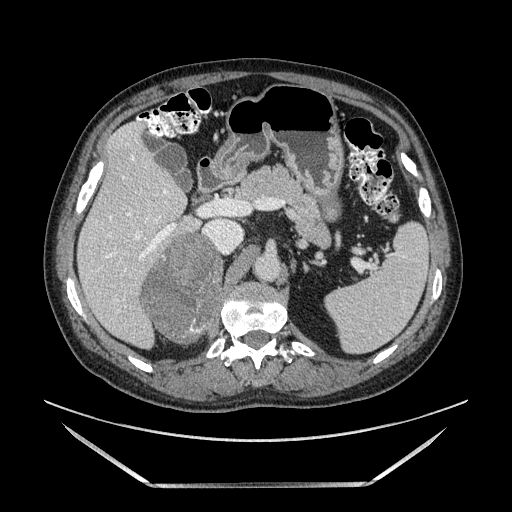
Contrast-enhanced abdominal CT, one axial slice. Position 88 of 185 along the scan axis. Soft-tissue window (W 400 / L 40 HU). 512 × 512 image matrix. Male patient. From the clinical record (not read from this slice): diagnosis: adrenocortical carcinoma; tumour side: right adrenal; tumour size at pathology: 10.3 cm; Ki-67 index: 20 %; stage (as recorded): 3.
Annotated regions visible in this slice (semi-automatically segmented with operator editing):
- mass: box from (x=142, y=233) to (x=226, y=344) px